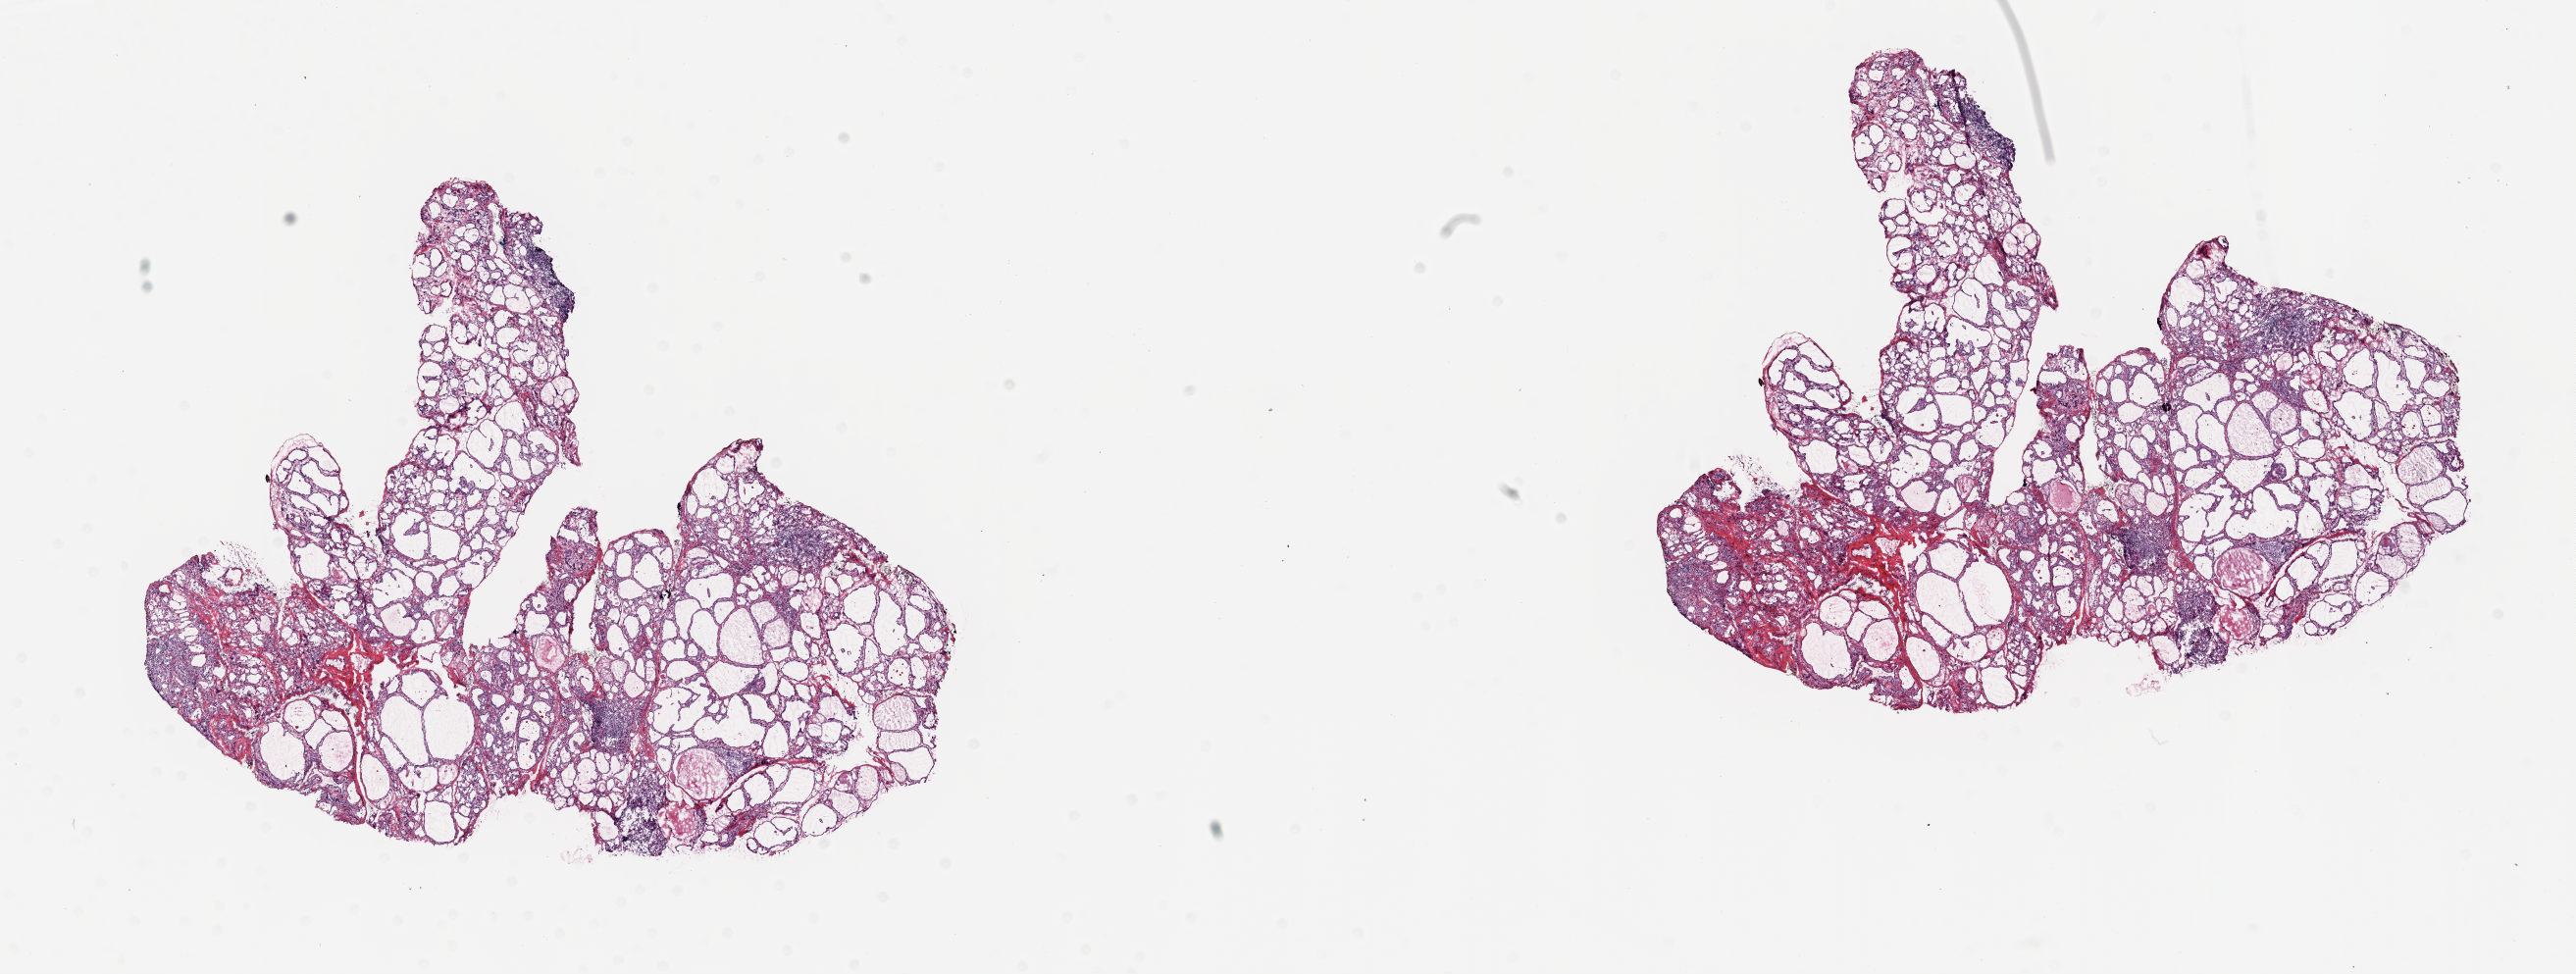
Whole-slide histology image, H&E-stained — a low-resolution overview of the entire scanned area, about 20.8 x 7.9 mm. Frozen section from the top of the tissue portion. Sample: solid tissue normal (non-tumour tissue), thyroid. Patient: male, age at initial diagnosis 25 years. Pathologist review of this section (percent, as recorded): tumour cells 0%, tumour nuclei 0%.
This section: solid tissue normal sample (biorepository sample class). Patient diagnosis: Papillary adenocarcinoma, NOS (thyroid gland).